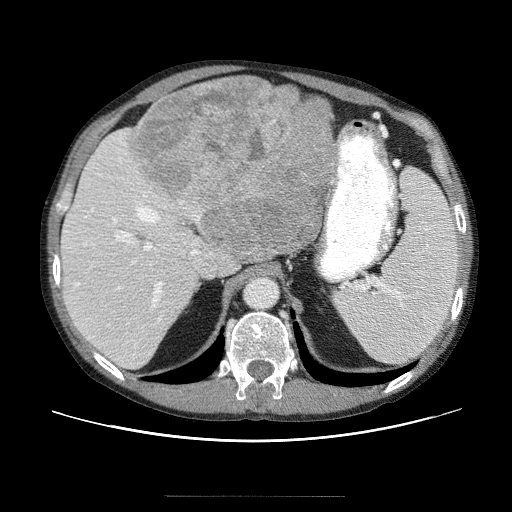
Contrast-enhanced abdominal CT (liver protocol), one axial slice. Slice 35 of 69 in the series (ordered by position). Reconstruction kernel STANDARD. Soft-tissue window (W 400 / L 40 HU). 2.5 mm slice thickness. 512 × 512 image matrix, field of view 380 × 380 mm. Case-level facts recorded for this patient, not image findings: diagnosis: hepatocellular carcinoma (patient treated with transarterial chemoembolisation; whether this scan precedes or follows treatment is not stated here); TNM stage (as recorded): Stage-IVB; Child-Pugh class: B.
Annotated regions visible in this slice (semi-automatically segmented with operator editing):
- abdominal aorta: bounding box <245,278,277,308> (left, top, right, bottom; pixels)
- liver parenchyma outside the tumour (the mass and vessels are separate outlines, so this box may not span the whole liver): <60,123,332,368>
- mass: <137,76,336,261>
- liver vessels: <78,163,215,343>